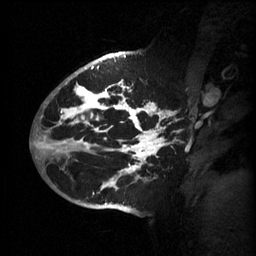
Breast MRI (dynamic contrast-enhanced), one sagittal slice; slice 39 of 60 in the series (ordered by position); 3 images stored at this slice position (order not interpretable as contrast timing); 1.5 T; TE 4.2 ms, TR 11 ms; 256 × 256 image matrix, field of view 220 × 220 mm. Female patient, age 51 years.
Annotated regions visible in this slice (semi-automatic segmentation, software-assisted and operator-edited):
- analysis volume of interest (the breast-tissue region the enhancement analysis was run in; not a lesion): bounding box <63,80,183,201> (left, top, right, bottom; pixels)
- tumour enhancement mask (voxels above the 70 % enhancement threshold inside the analysis volume of interest): <63,80,178,193>